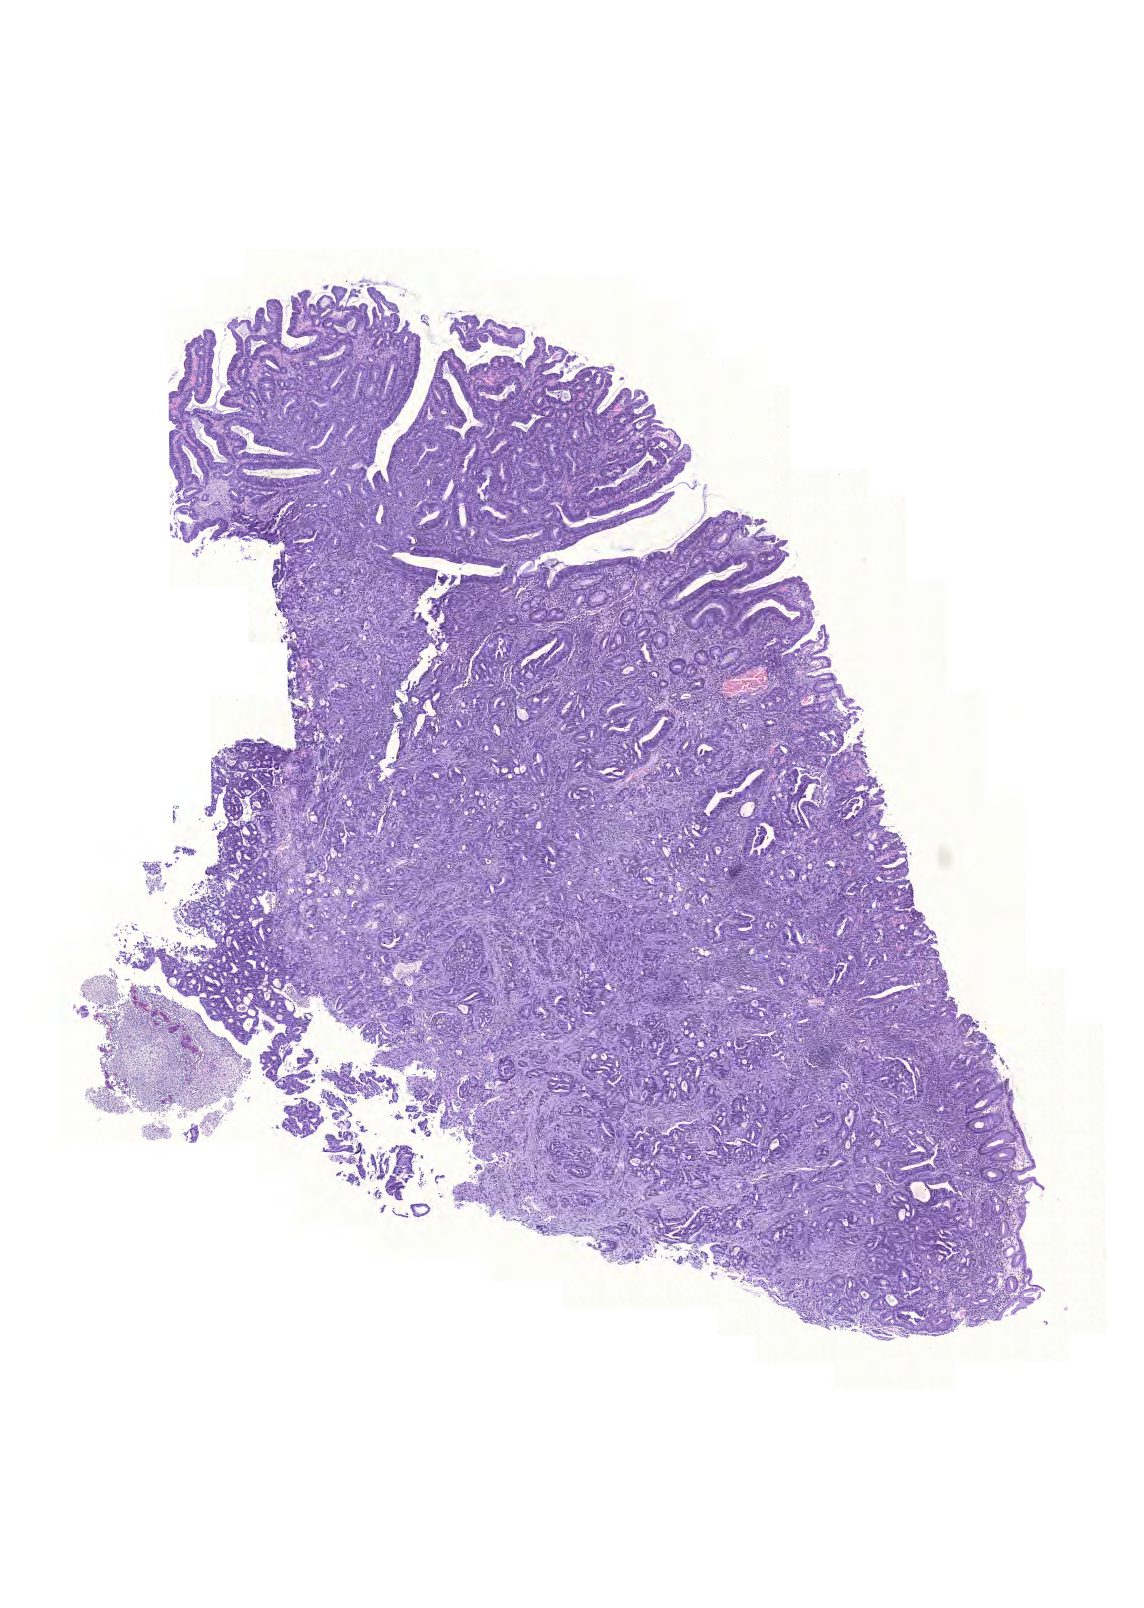
Digitized H&E tissue section (whole slide) — whole scanned area (about 8.5 x 12.0 mm, acquisition: 20x scan) shown as a low-resolution overview, FFPE section, primary tumour sample from the colon. Male, age 67 years at initial diagnosis.
* TNM: T3 N0 M0
* pathologic diagnosis: Adenocarcinoma, NOS (ascending colon)
* AJCC pathologic stage: IIA